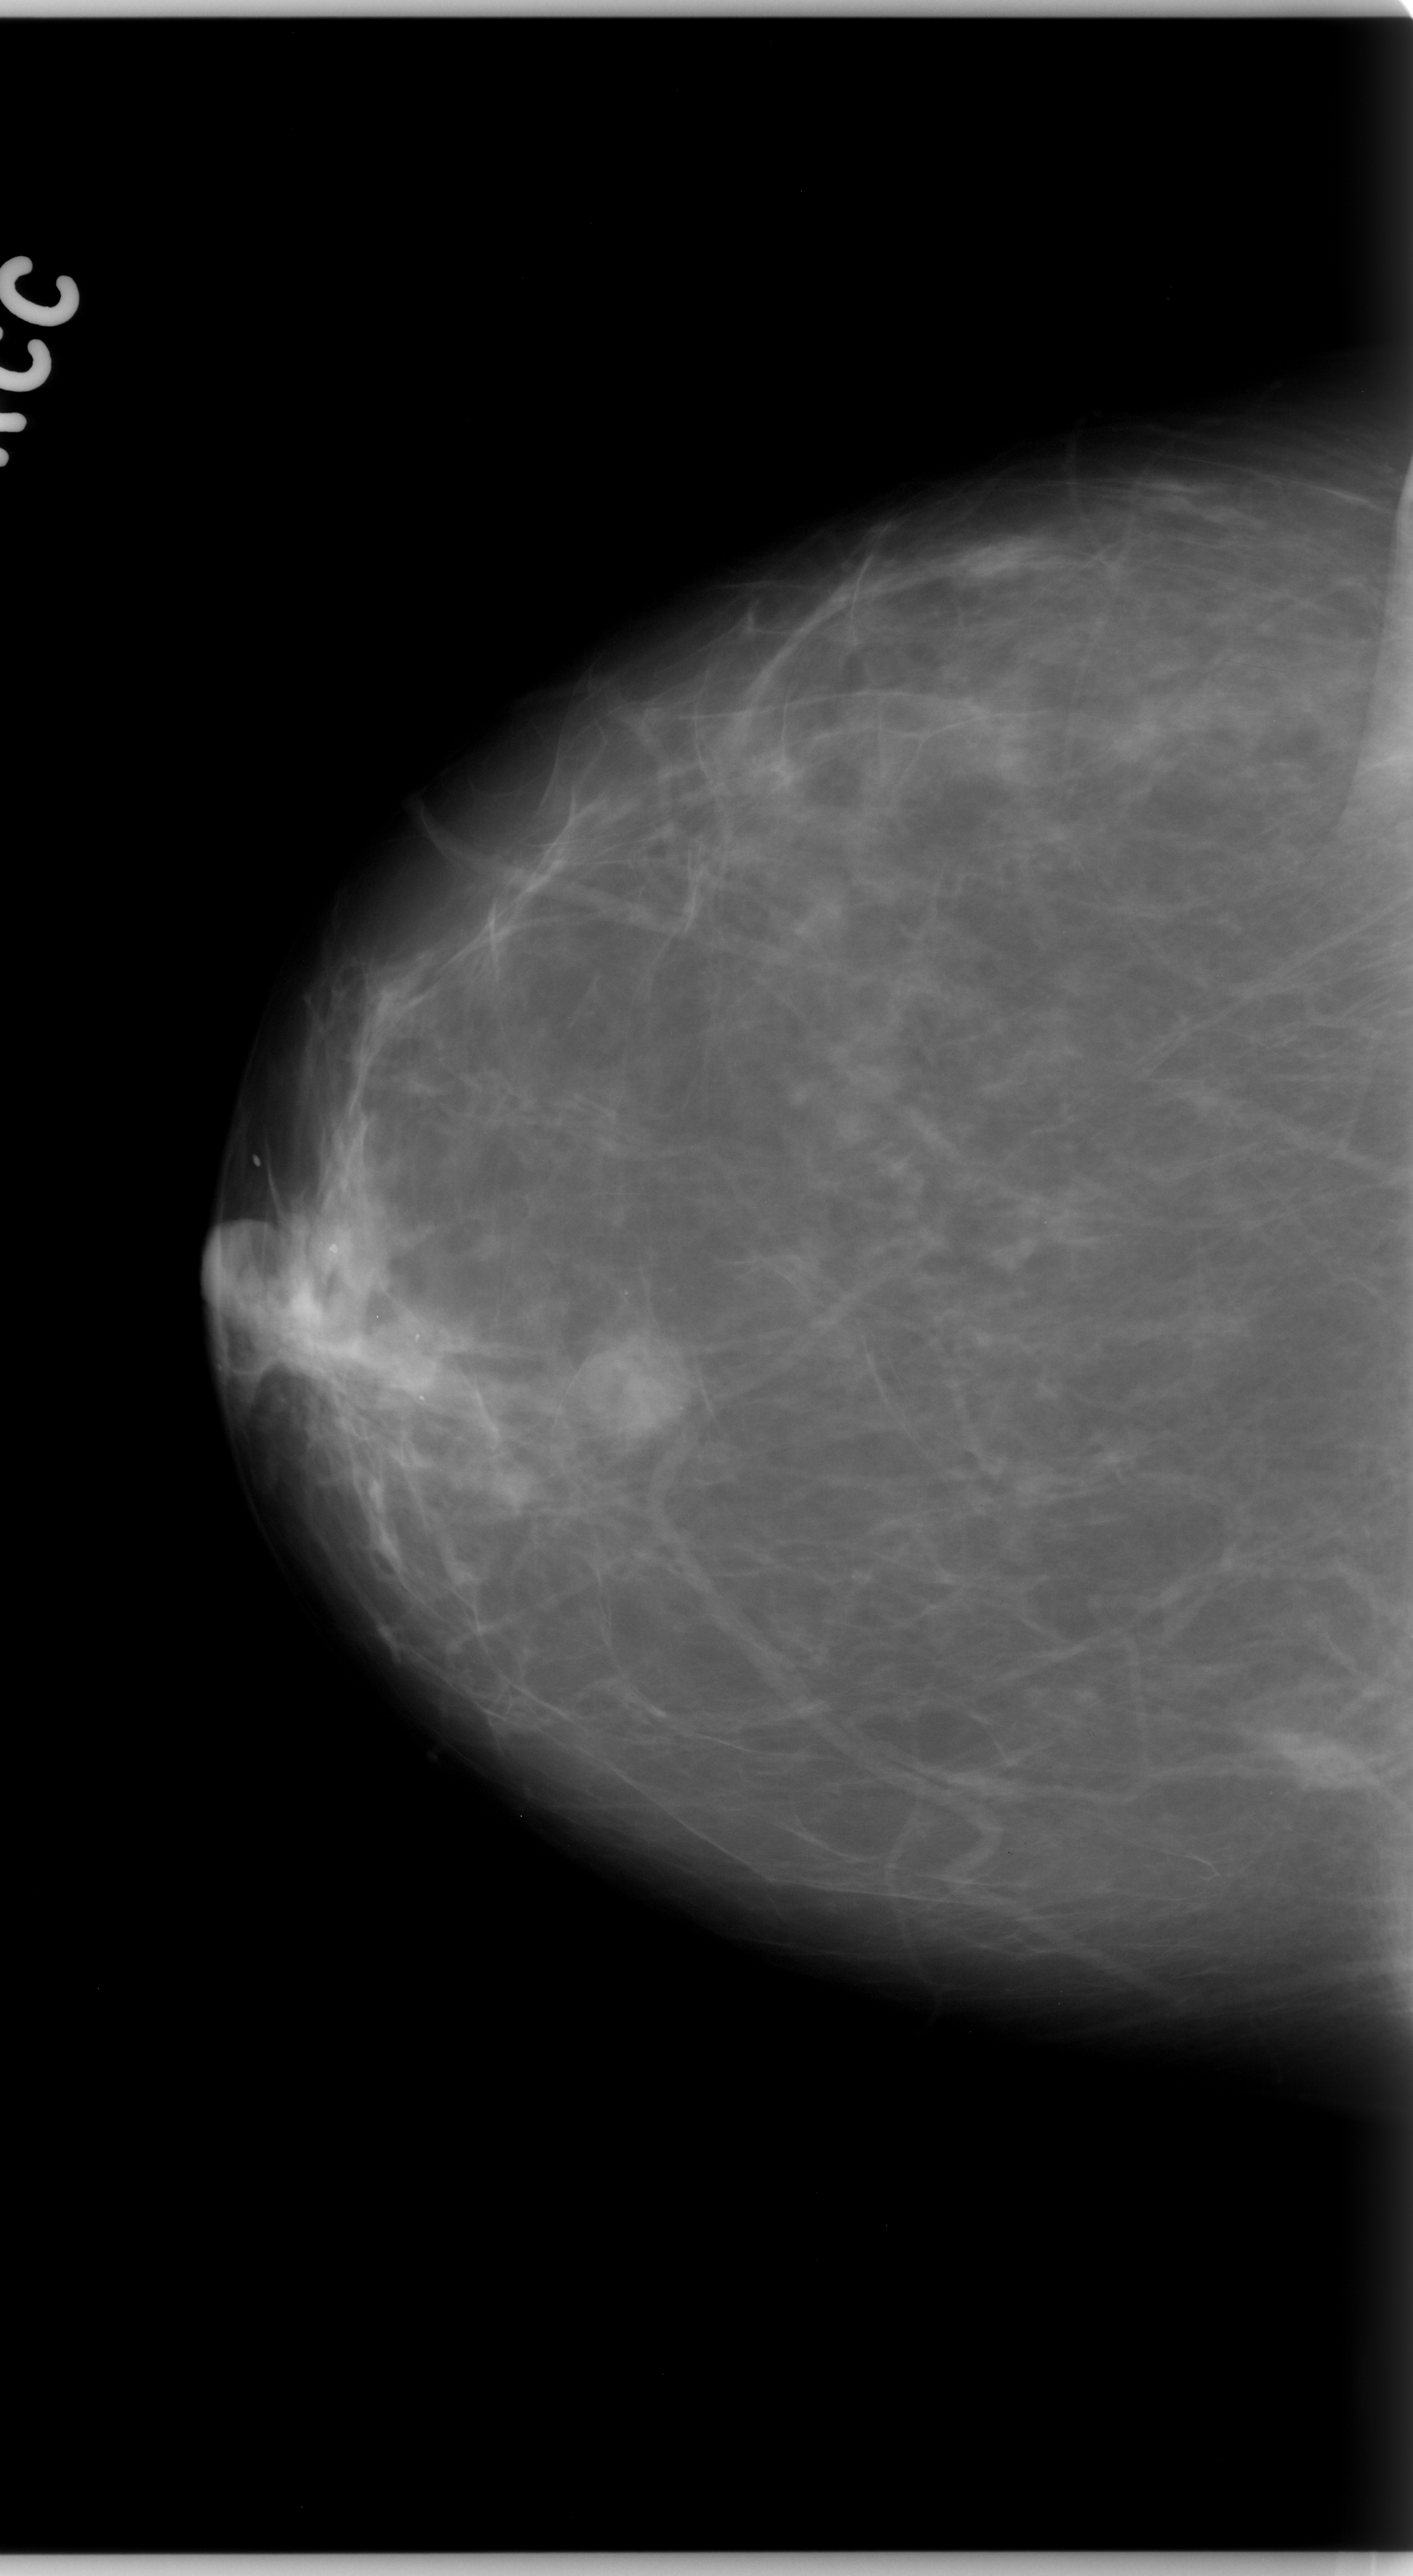
Digitized screen-film mammogram; right breast; craniocaudal (CC) view; breast composition: almost entirely fatty (BI-RADS density category 1 of 4).
Finding: mass, shape round, margins microlobulated; BI-RADS assessment category 4; pathology (as recorded): malignant.